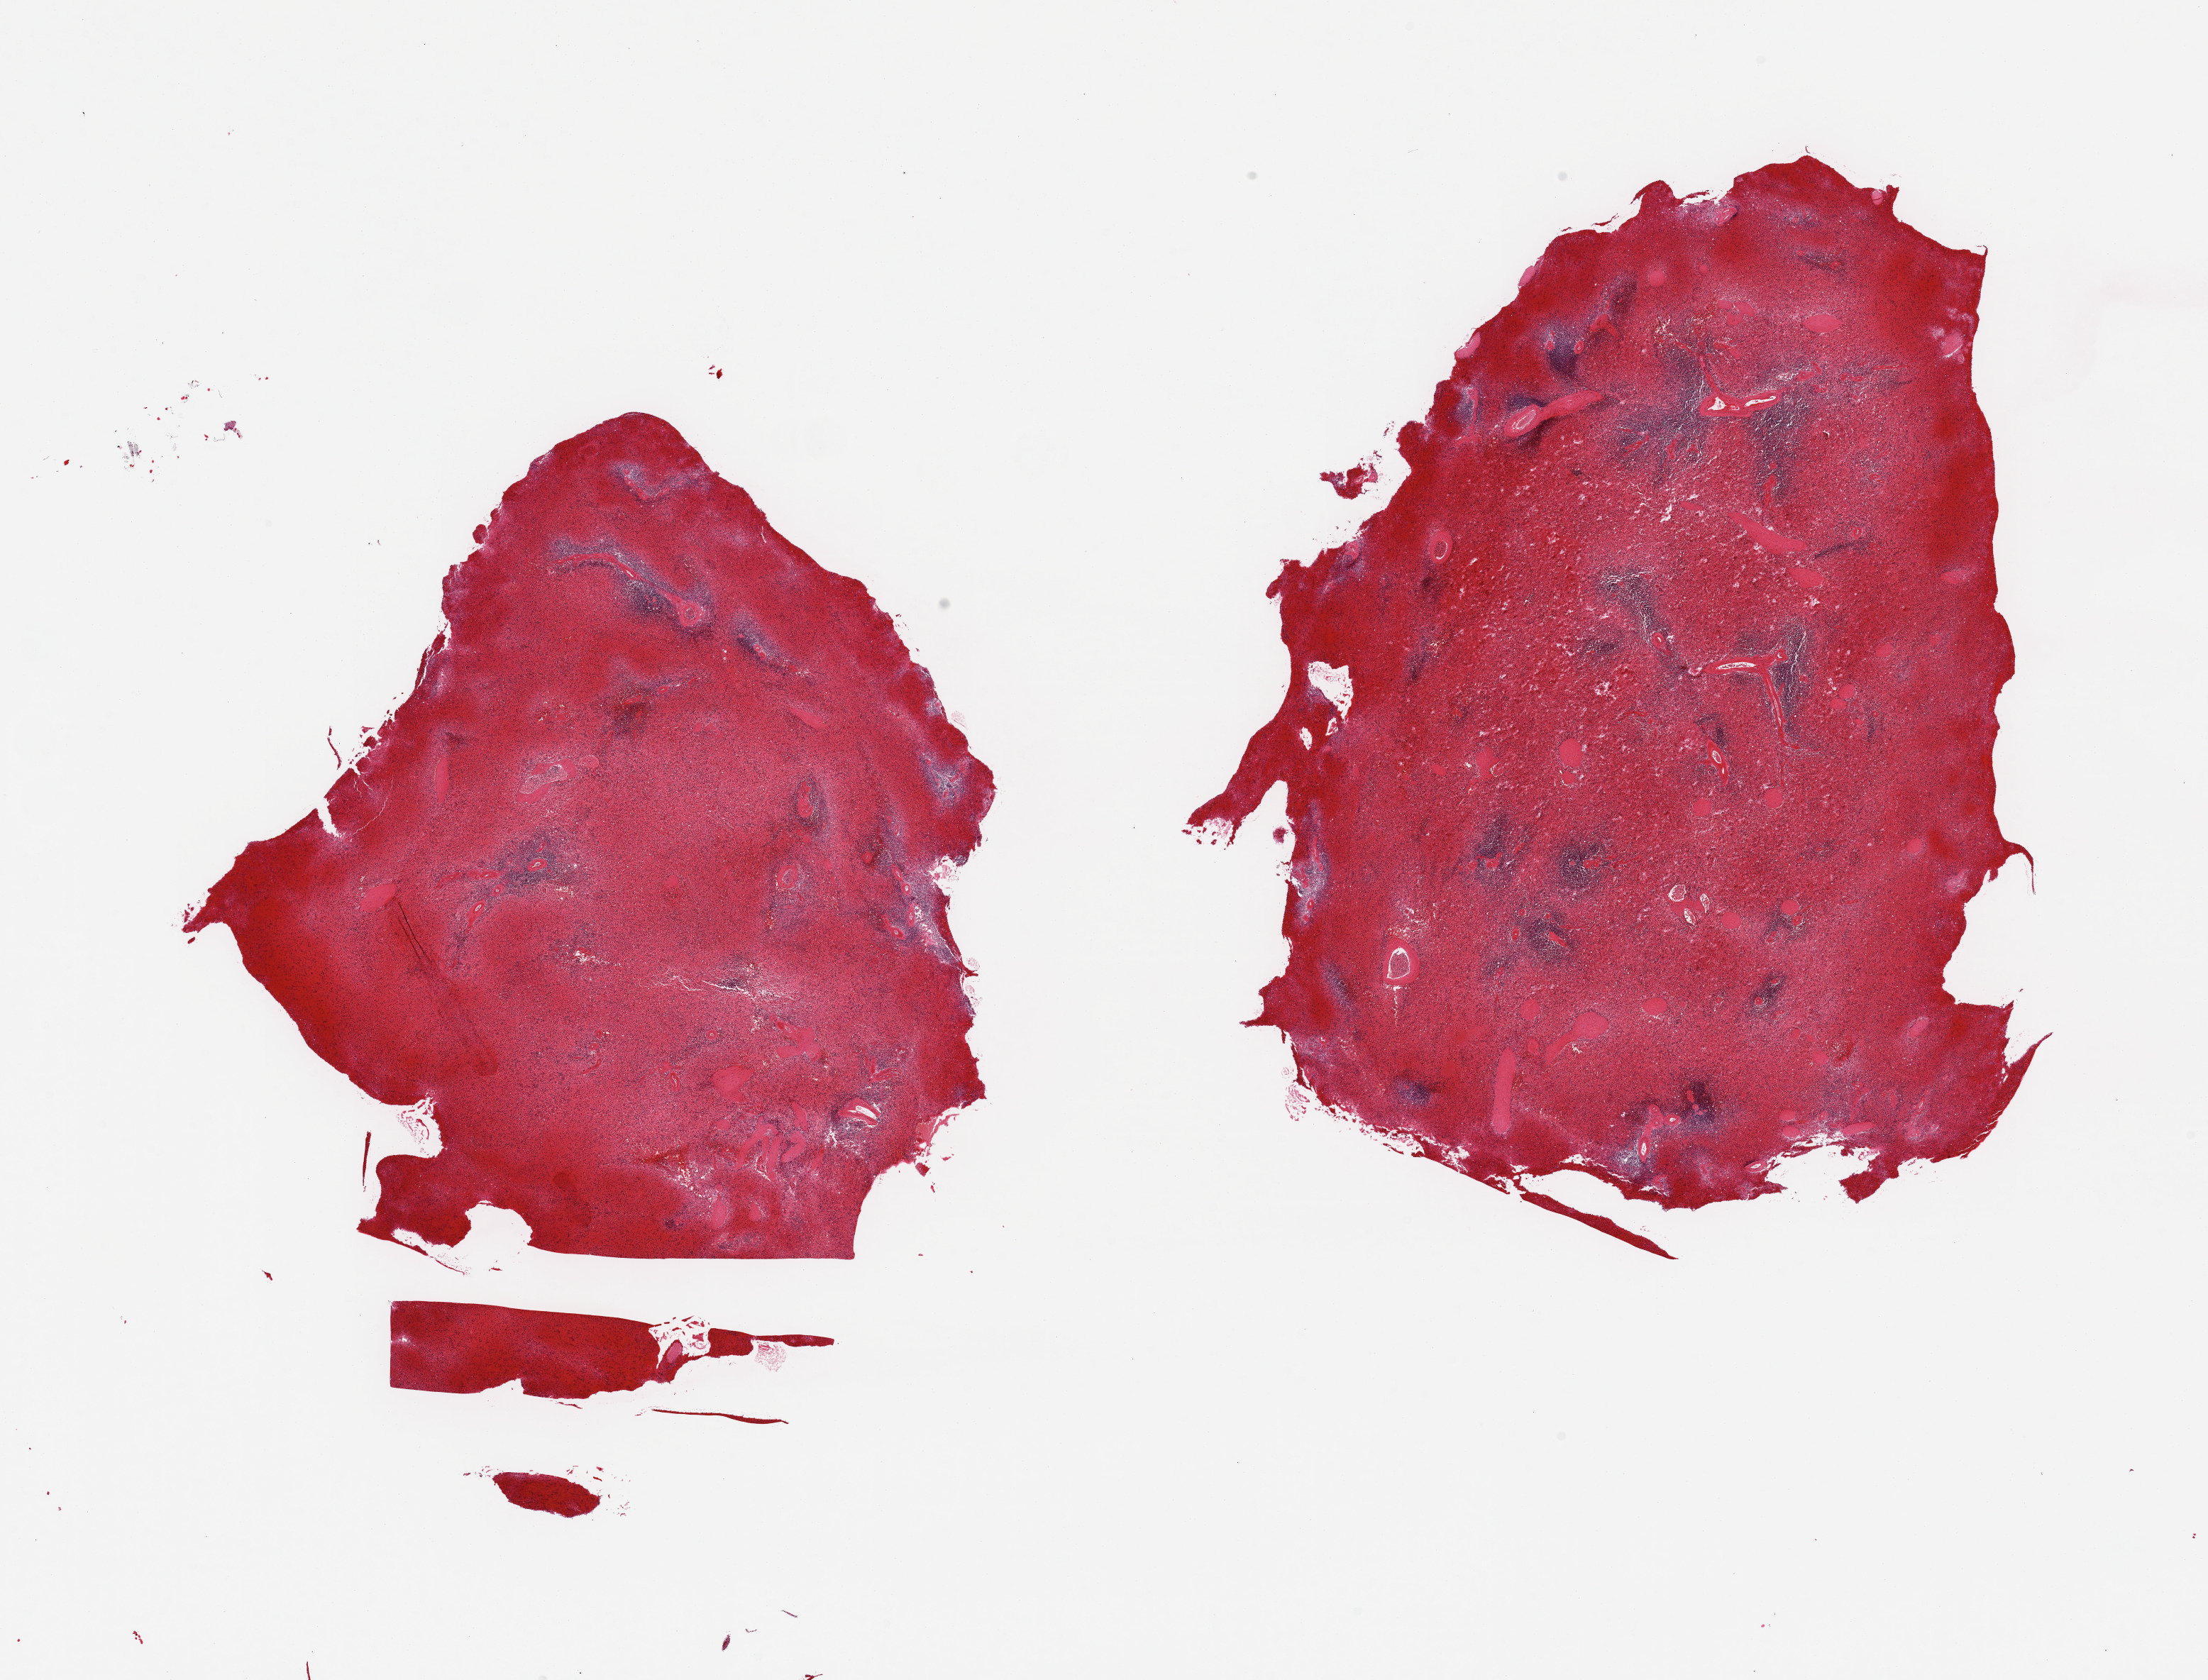
Digitized hematoxylin and eosin (H&E)-stained section, whole scanned area (about 24.6 x 18.7 mm) shown as a low-resolution overview; PAXgene-fixed, paraffin-embedded tissue; sampled site (target tissue): spleen; donor tissue sample. Donor: male.
Pathologist's review note for this sample: 2 pieces, marked congestion.